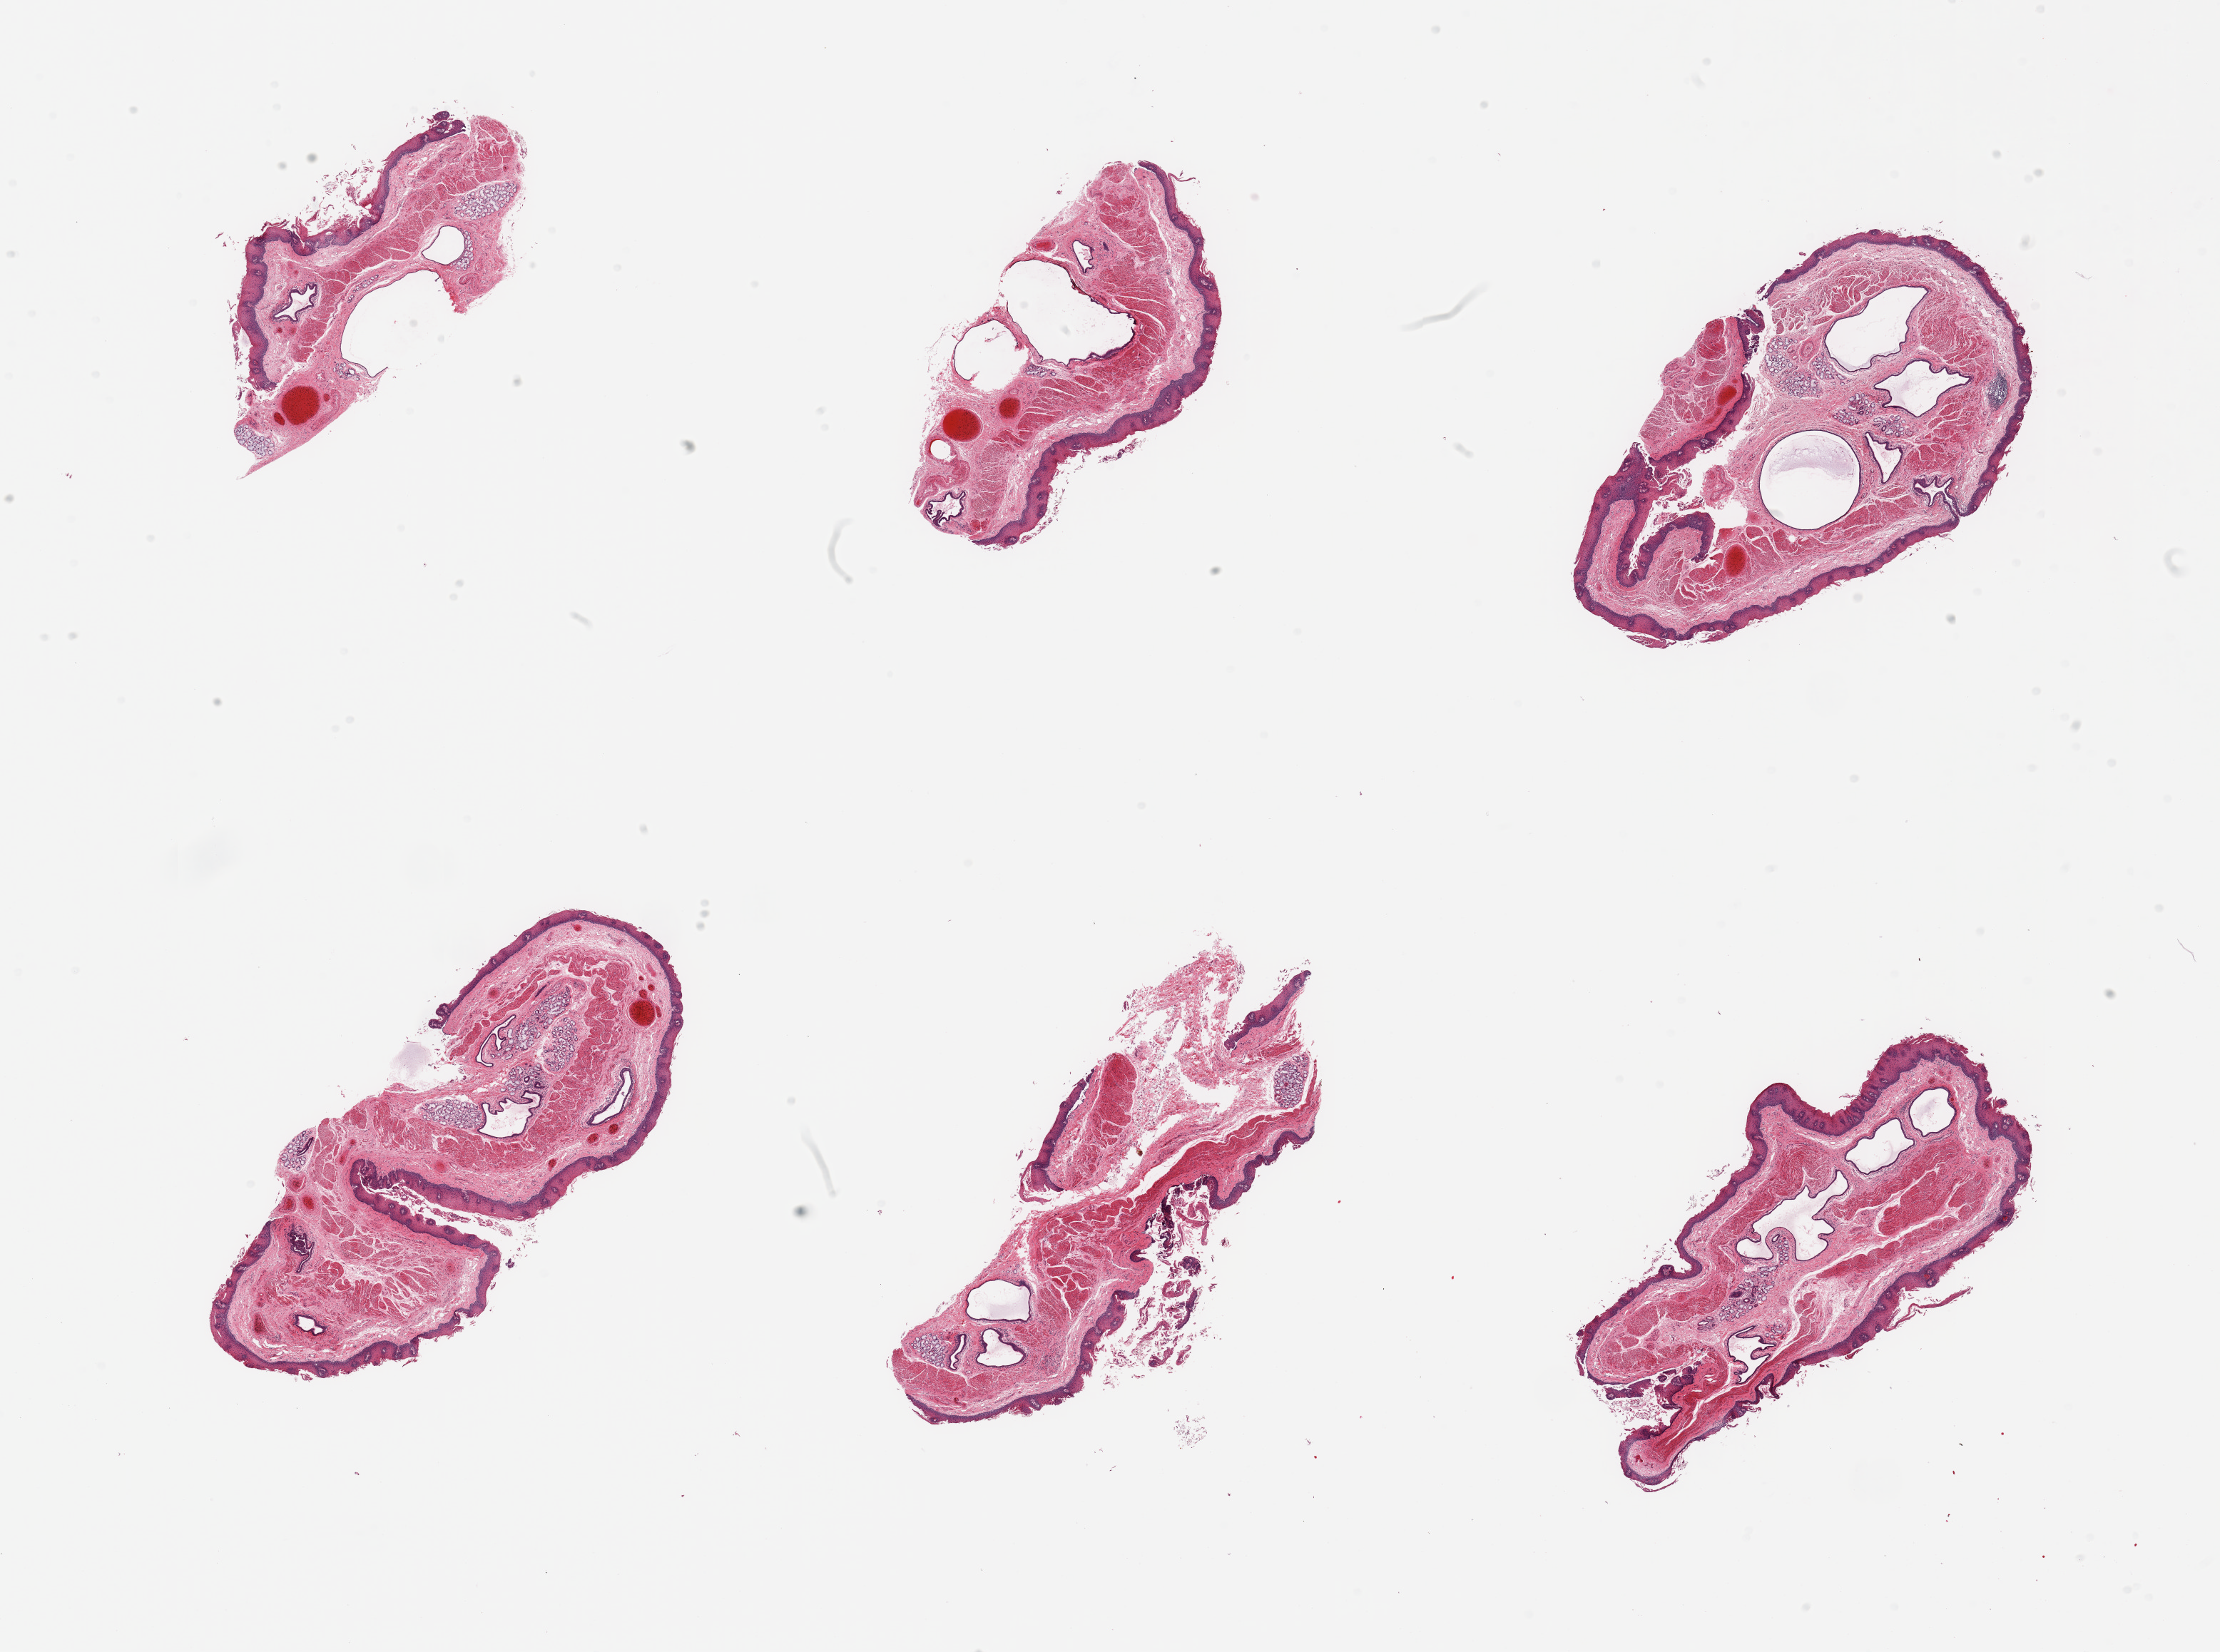
Hematoxylin and eosin (H&E) whole-slide image, whole scanned area (about 24.6 x 18.3 mm) shown as a low-resolution overview; PAXgene-fixed, paraffin-embedded tissue; section of esophageal mucous membrane (target tissue); tissue donor sample. Male donor.
Review note (as recorded): 6 pieces, squamous mucosa up to ~0.25mm, submucosal mucus glands present; Superficial early sloughing.